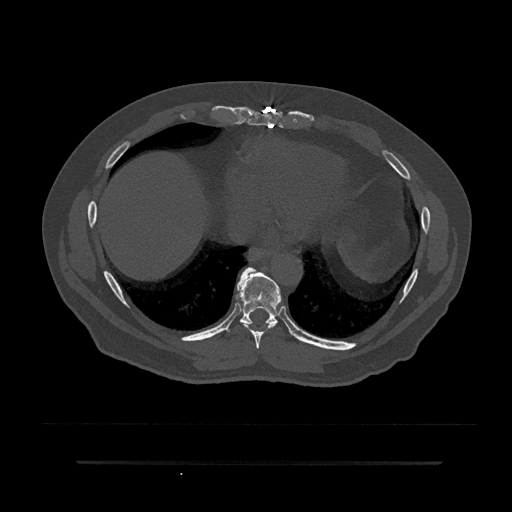
CT including the spine, one axial slice. Position 401 of 797 along the scan axis. Reconstruction kernel Br40s/3. 120 kVp. Bone window (W 1800 / L 400 HU). 0.5 mm slice thickness. 512 × 512 image matrix, field of view 464 × 464 mm. Male patient, age 59 years. Case-level facts recorded for this patient, not image findings: primary cancer: bile ducts; vertebrae with lytic lesions (as recorded): T10.
Annotated regions visible in this slice (semi-automatically segmented with operator editing):
- T8 vertebra: bounding box <244,324,275,350> (left, top, right, bottom; pixels)
- T9 vertebra: <227,267,282,332>